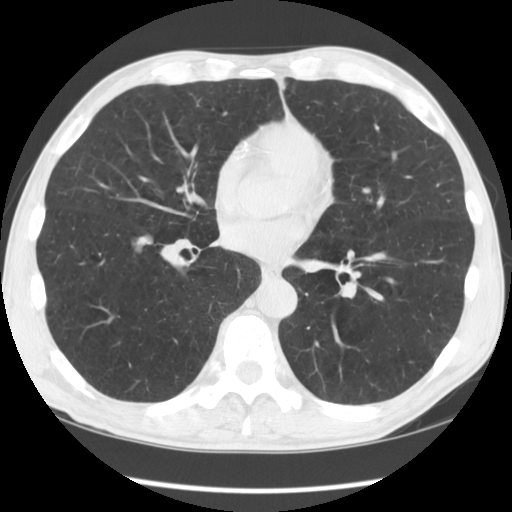
Low-dose screening chest CT, one axial slice; slice 53 of 135 in the series (ordered by position); reconstruction kernel STANDARD; 120 kVp; lung window (W 1500 / L -600 HU); 2.5 mm slice thickness; 512 × 512 image matrix, field of view 360 × 360 mm.
Structures marked on this image (expert manual segmentation):
- lesion 1 (tumor, lower lobe of right lung): bounding box (x1, y1, x2, y2) in pixels: (135, 236, 153, 251)